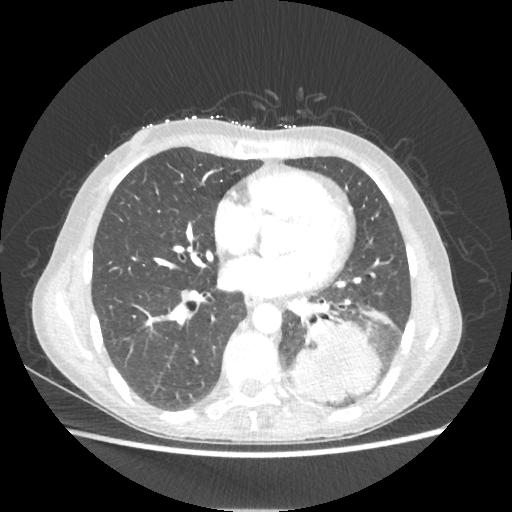
Chest CT, one axial slice; slice 97 of 221 in the series (ordered by position); reconstruction kernel STANDARD; lung window (W 1500 / L -600 HU); 1.25 mm slice thickness; 512 × 512 image matrix, field of view 360 × 360 mm. Patient: female, 53 years. Case-level facts recorded for this patient, not image findings: clinical TNM (as recorded): T3 N0 M0.
Outlined on this slice (bounding box drawn by a radiologist):
- lung tumour (recorded histology: adenocarcinoma): box from (x=288, y=318) to (x=381, y=402) px